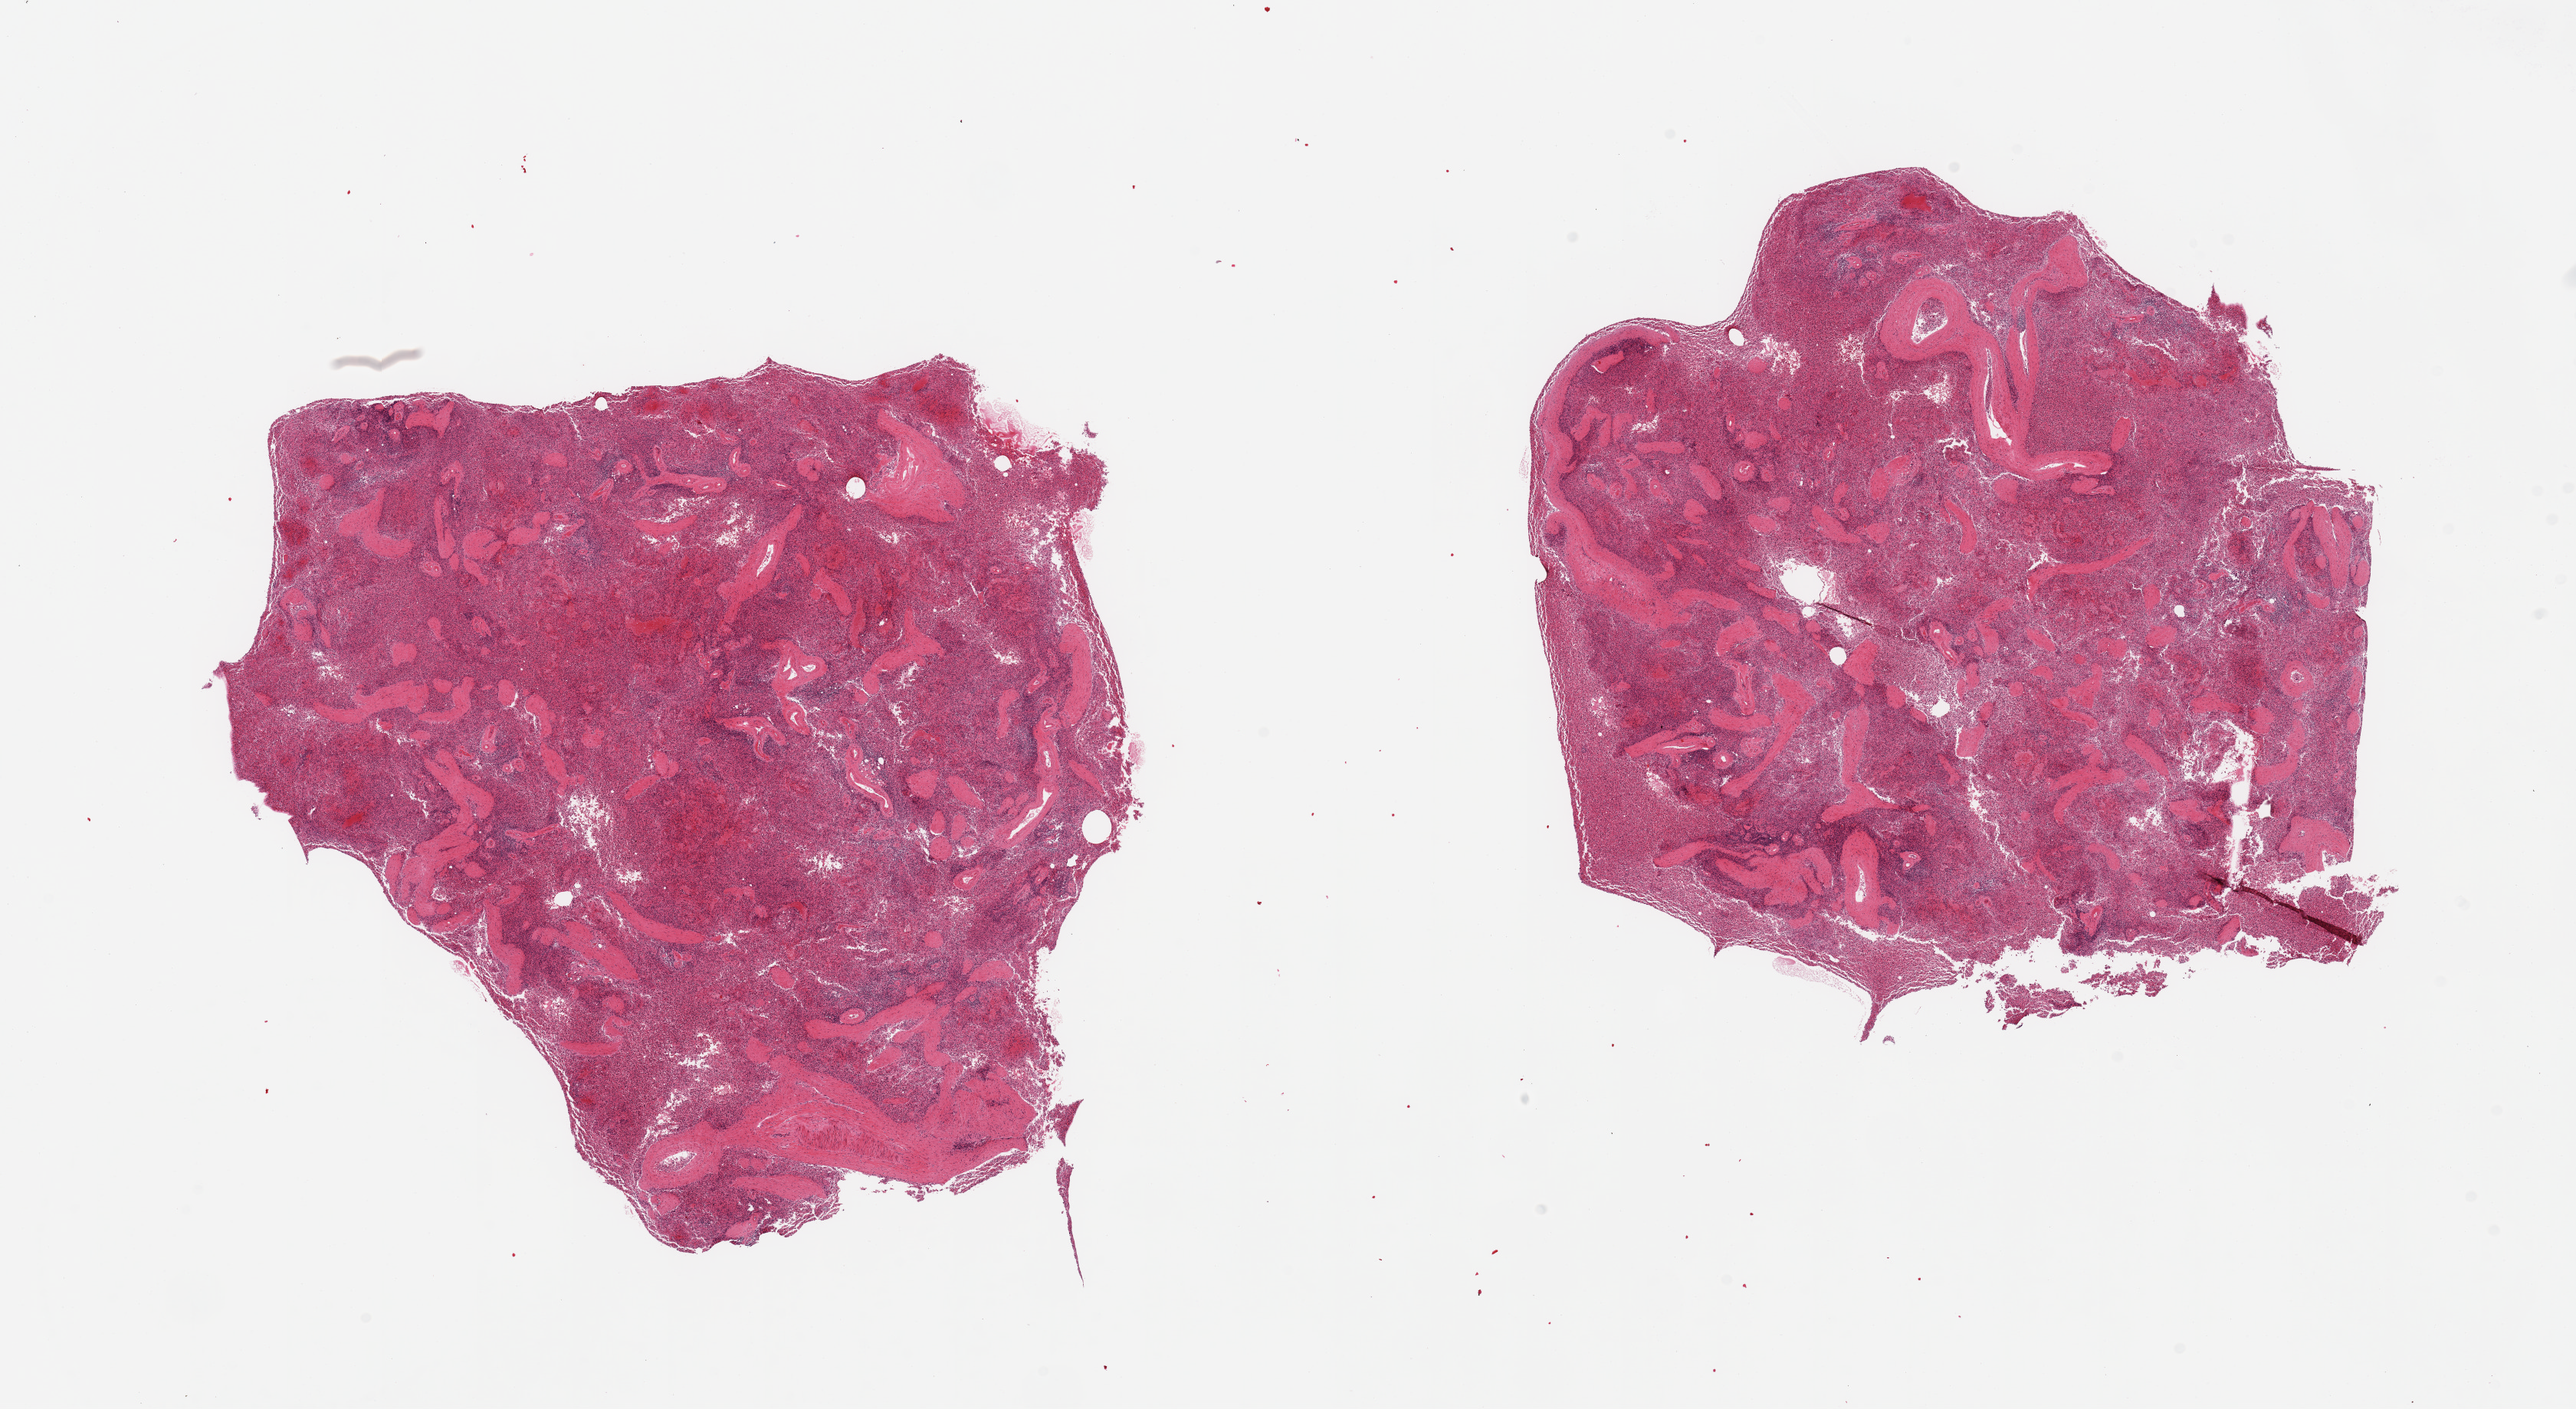
Digitized haematoxylin and eosin-stained section, low-resolution overview of the scanned area, about 26.6 x 14.5 mm; PAXgene-fixed paraffin-embedded (PFPE) section; target tissue: spleen; donor tissue sample. Donor sex: male.
Pathologist's review note for this sample: 2 pieces; congested.